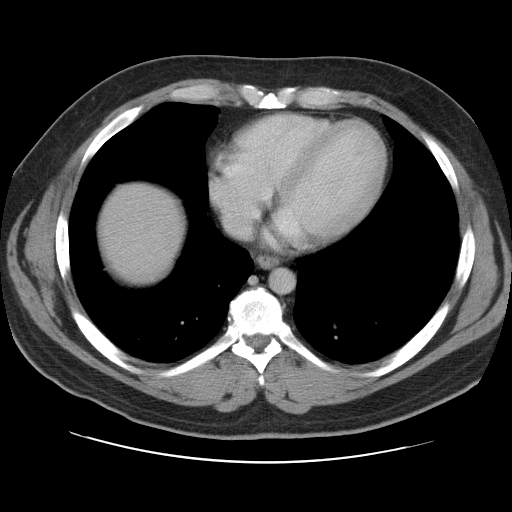
Contrast-enhanced abdominal CT, one axial slice; position 104 of 109 along the scan axis; 120 kVp; intravenous contrast given; soft-tissue window (W 400 / L 40 HU); 5 mm slice thickness; 512 × 512 image matrix. Male patient, age 35 years. Case-level facts recorded for this patient, not image findings: diagnosis: colorectal cancer liver metastases, imaged before liver resection; multiple liver metastases: yes; largest metastasis: 2.8 cm.
Annotated regions visible in this slice (manually delineated by an expert):
- liver: bounding box <98,182,183,285> (left, top, right, bottom; pixels)
- planned liver remnant (the part of the liver to remain after resection): <98,182,183,284>